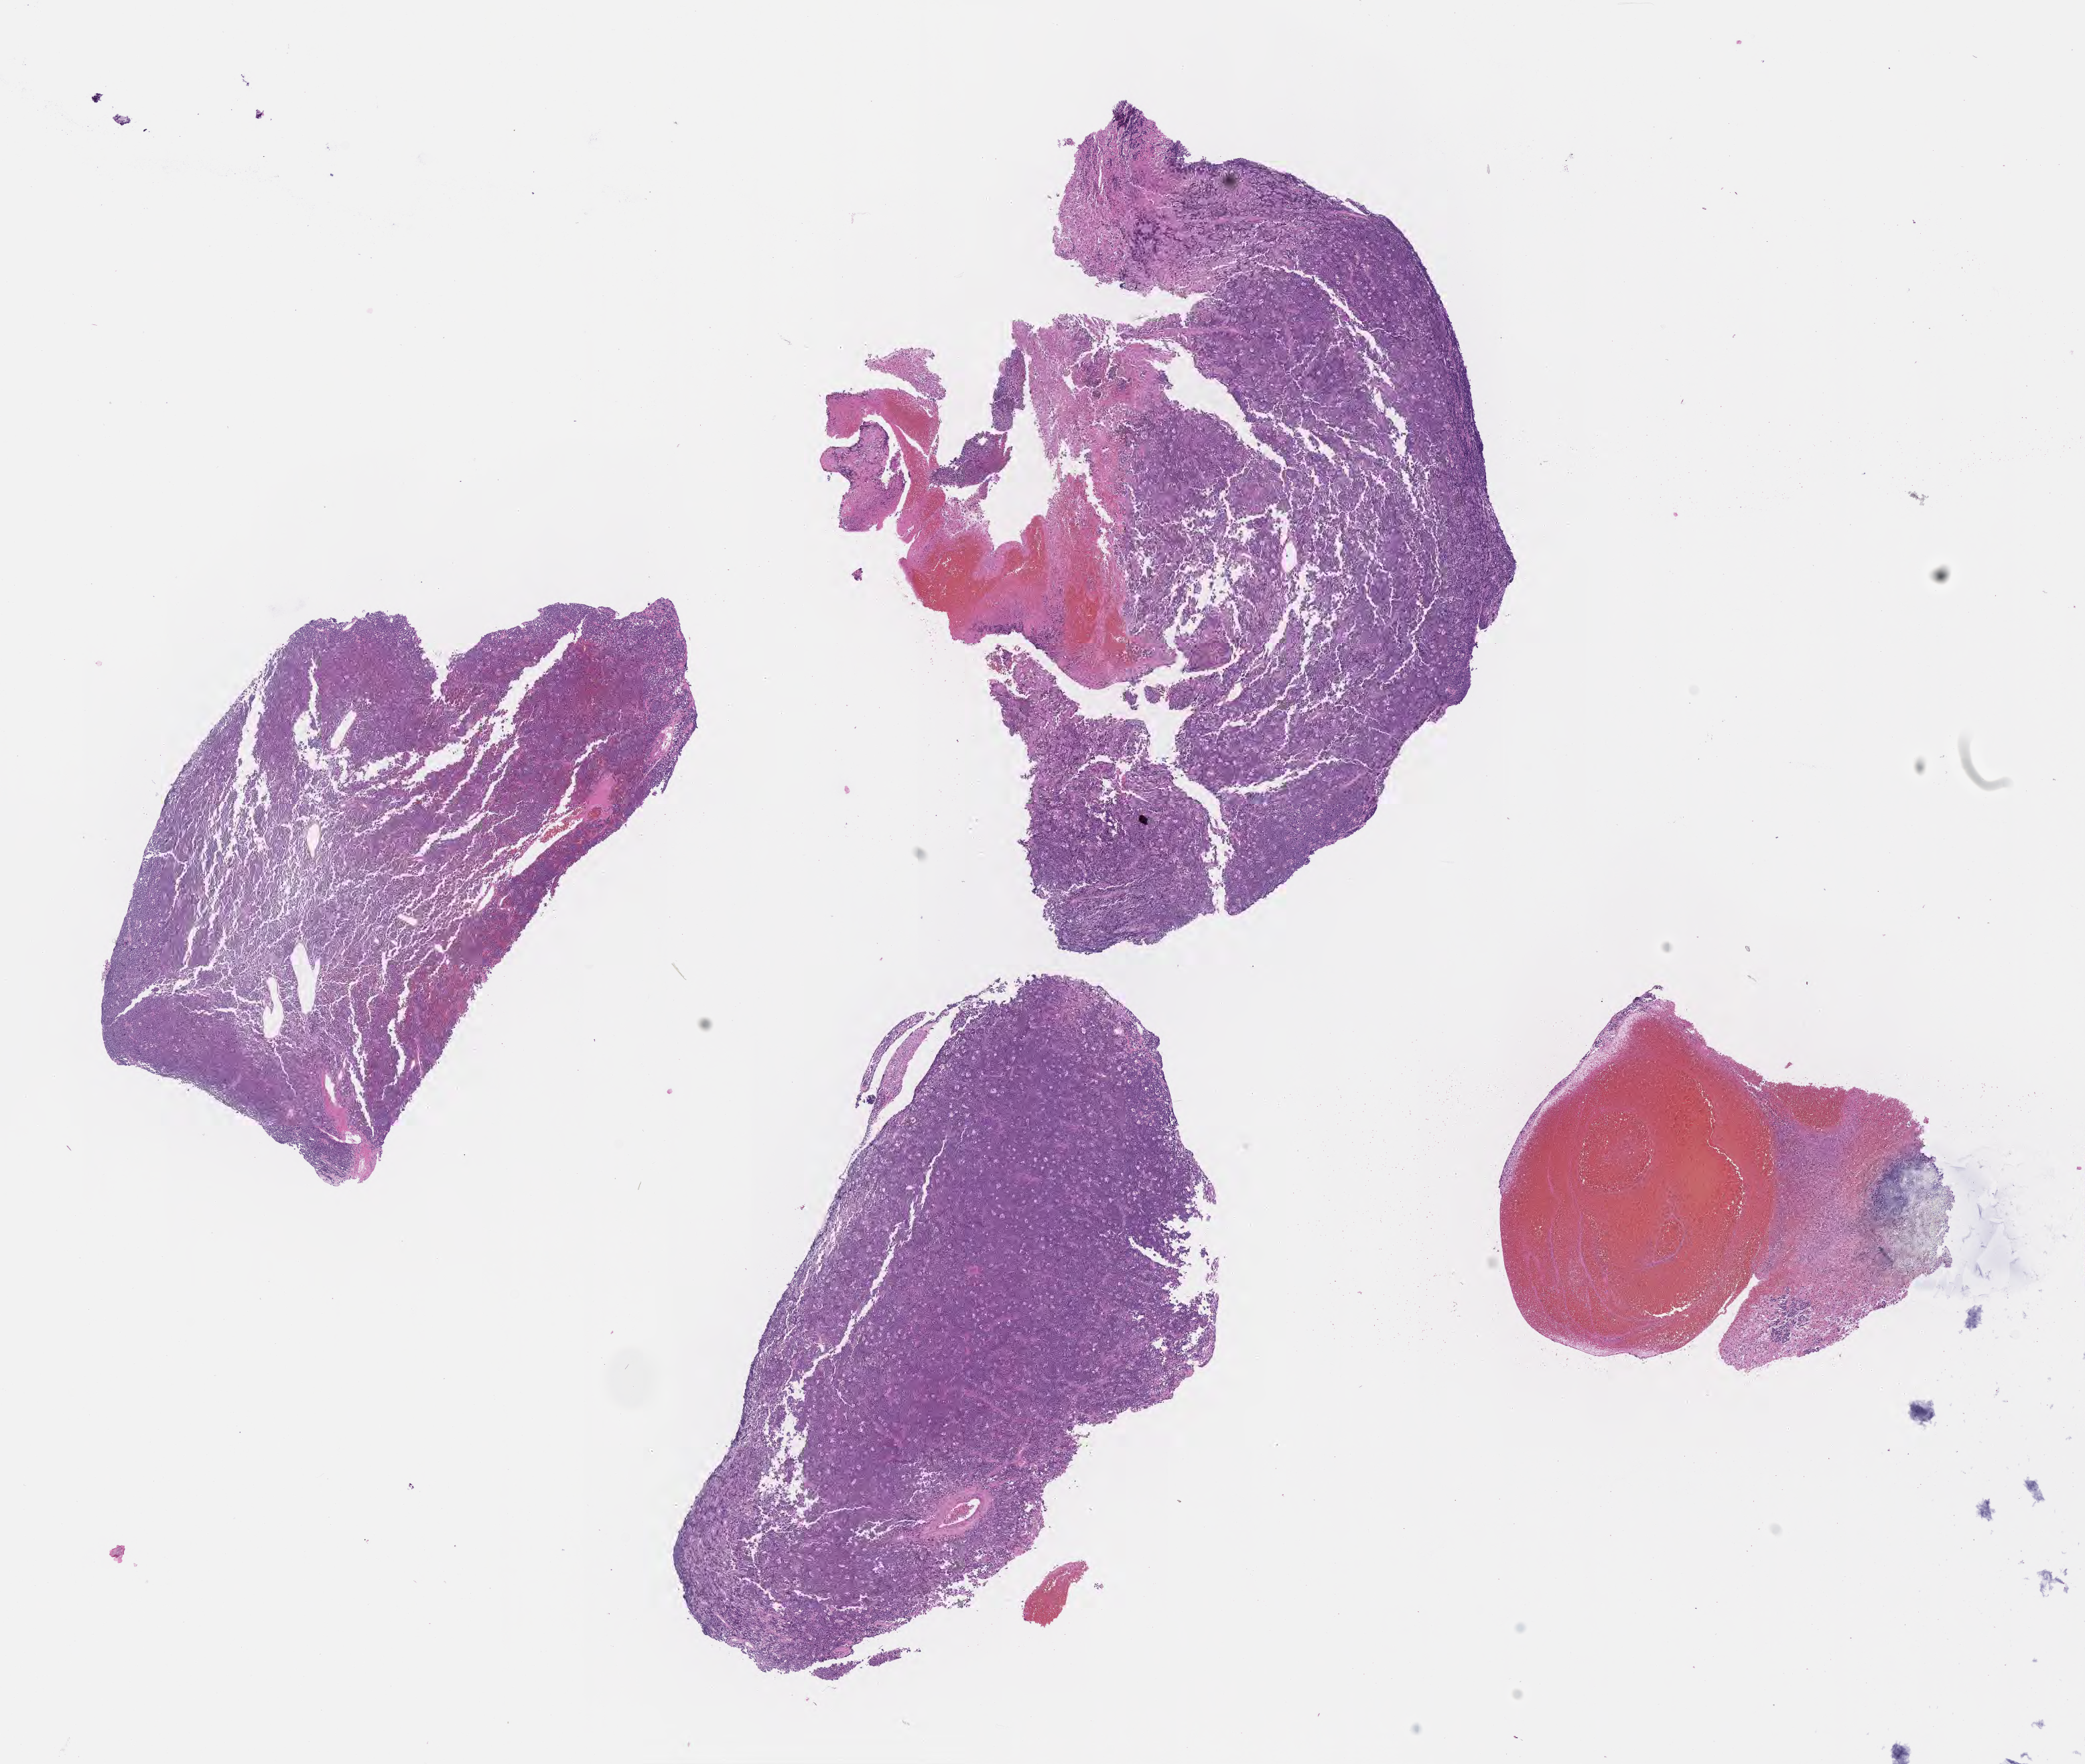
Hematoxylin and eosin (H&E) whole-slide image, low-resolution overview of the scanned area, about 12.6 x 10.6 mm. Tumor tissue. Male patient, aged 10.
• histologic diagnosis: Burkitt lymphoma, NOS